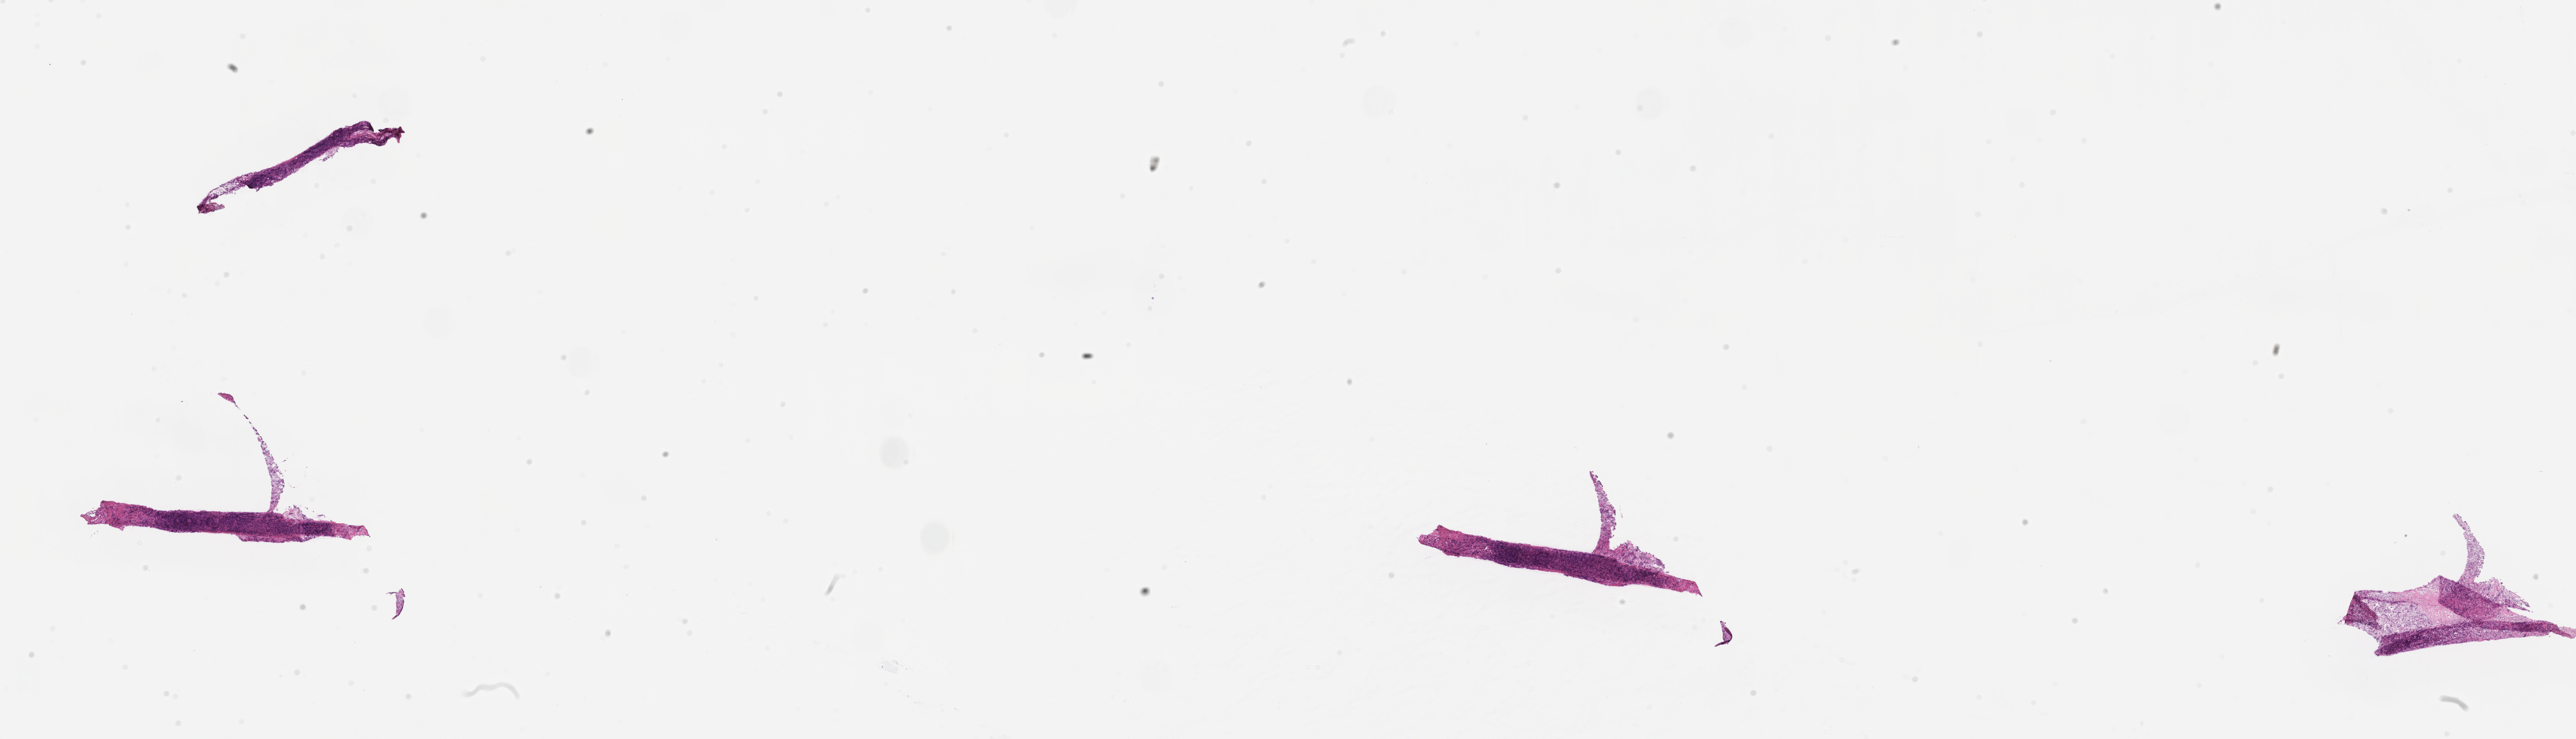
Whole-slide image, haematoxylin and eosin stain — shown as a low-resolution overview of the whole scanned area (about 32.6 x 9.4 mm); cryosection; primary tumor; anatomic site: breast (right). Female patient; age at initial diagnosis 61 years. Slide review estimates, as recorded: tumor cells 85%, tumor nuclei 85%, stromal cells 15%, necrosis 0%, normal cells 0%. Infiltration values recorded for this section: lymphocyte infiltration 4%, monocyte infiltration 2%, neutrophil infiltration 4%.
Histologic diagnosis: Infiltrating duct carcinoma, NOS.